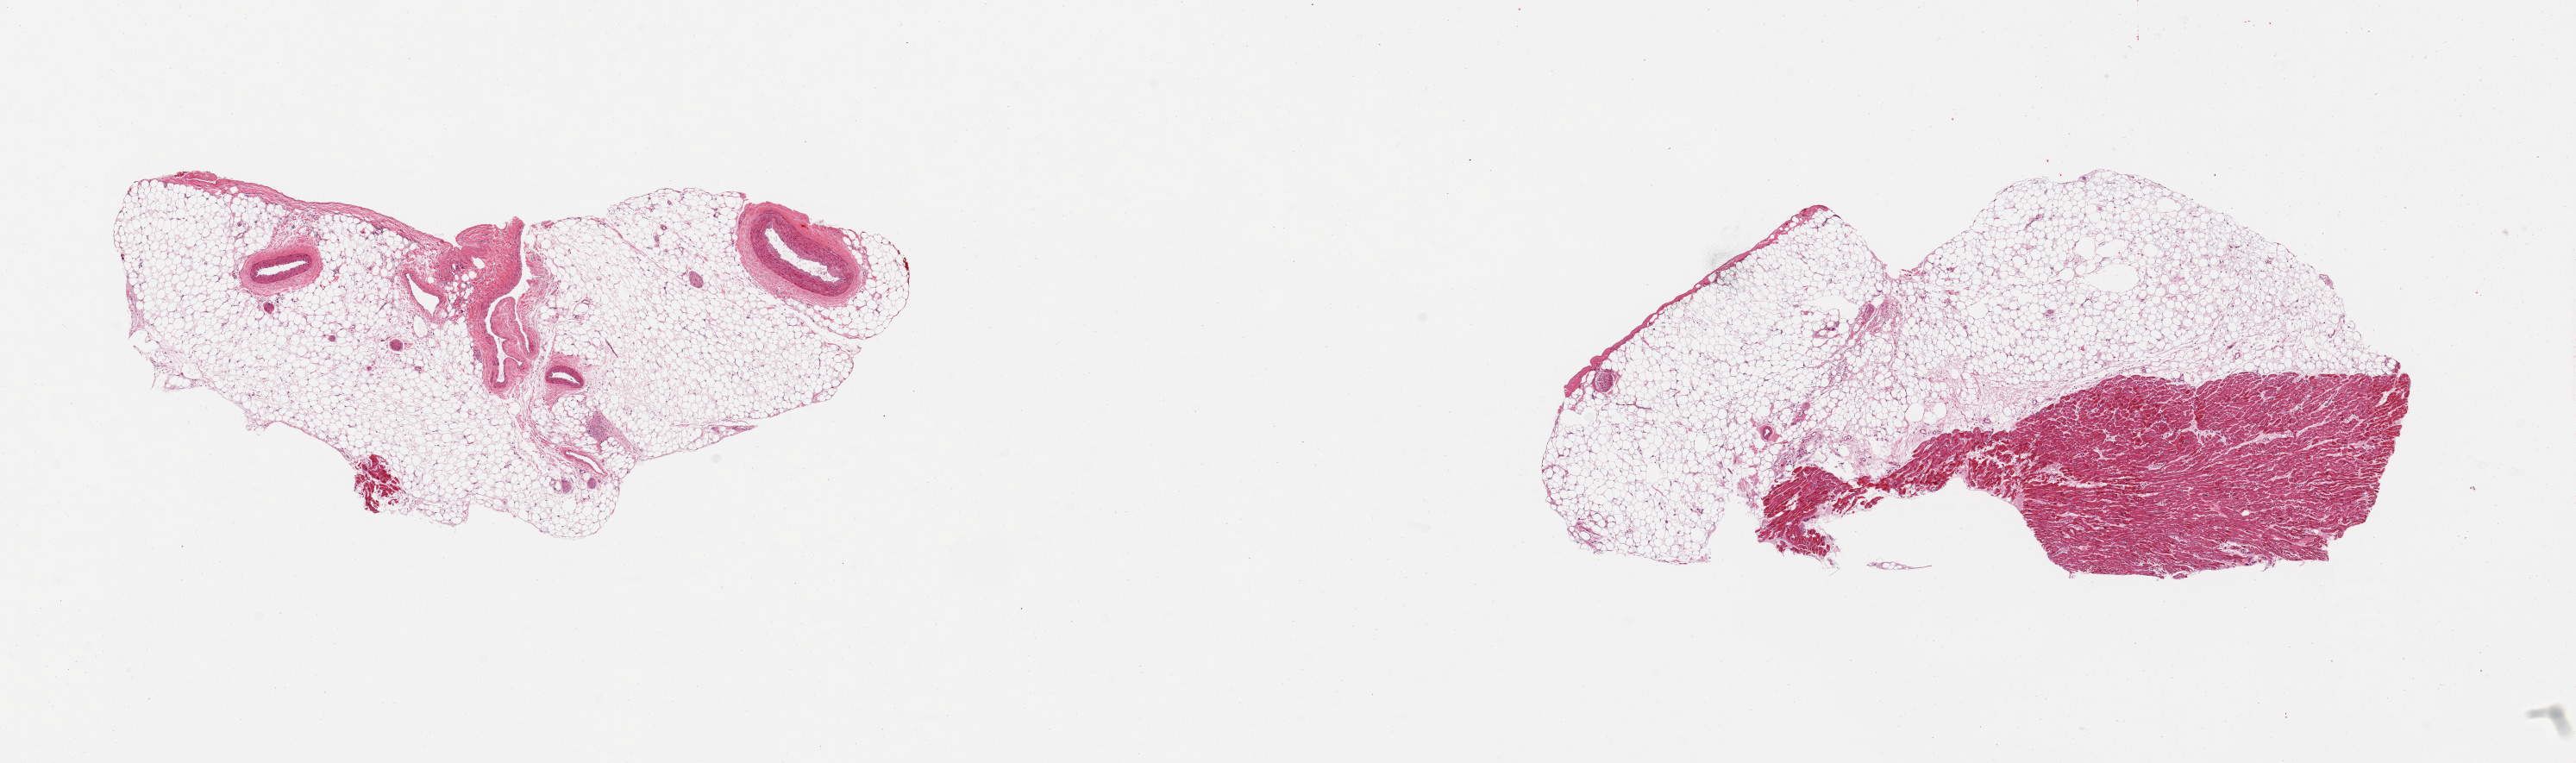
H&E whole-slide image, whole scanned area (about 23.6 x 7.0 mm) shown as a low-resolution overview.
Specimen: PAXgene-fixed paraffin-embedded (PFPE) section; sampled site (target tissue): coronary artery; donor tissue sample.